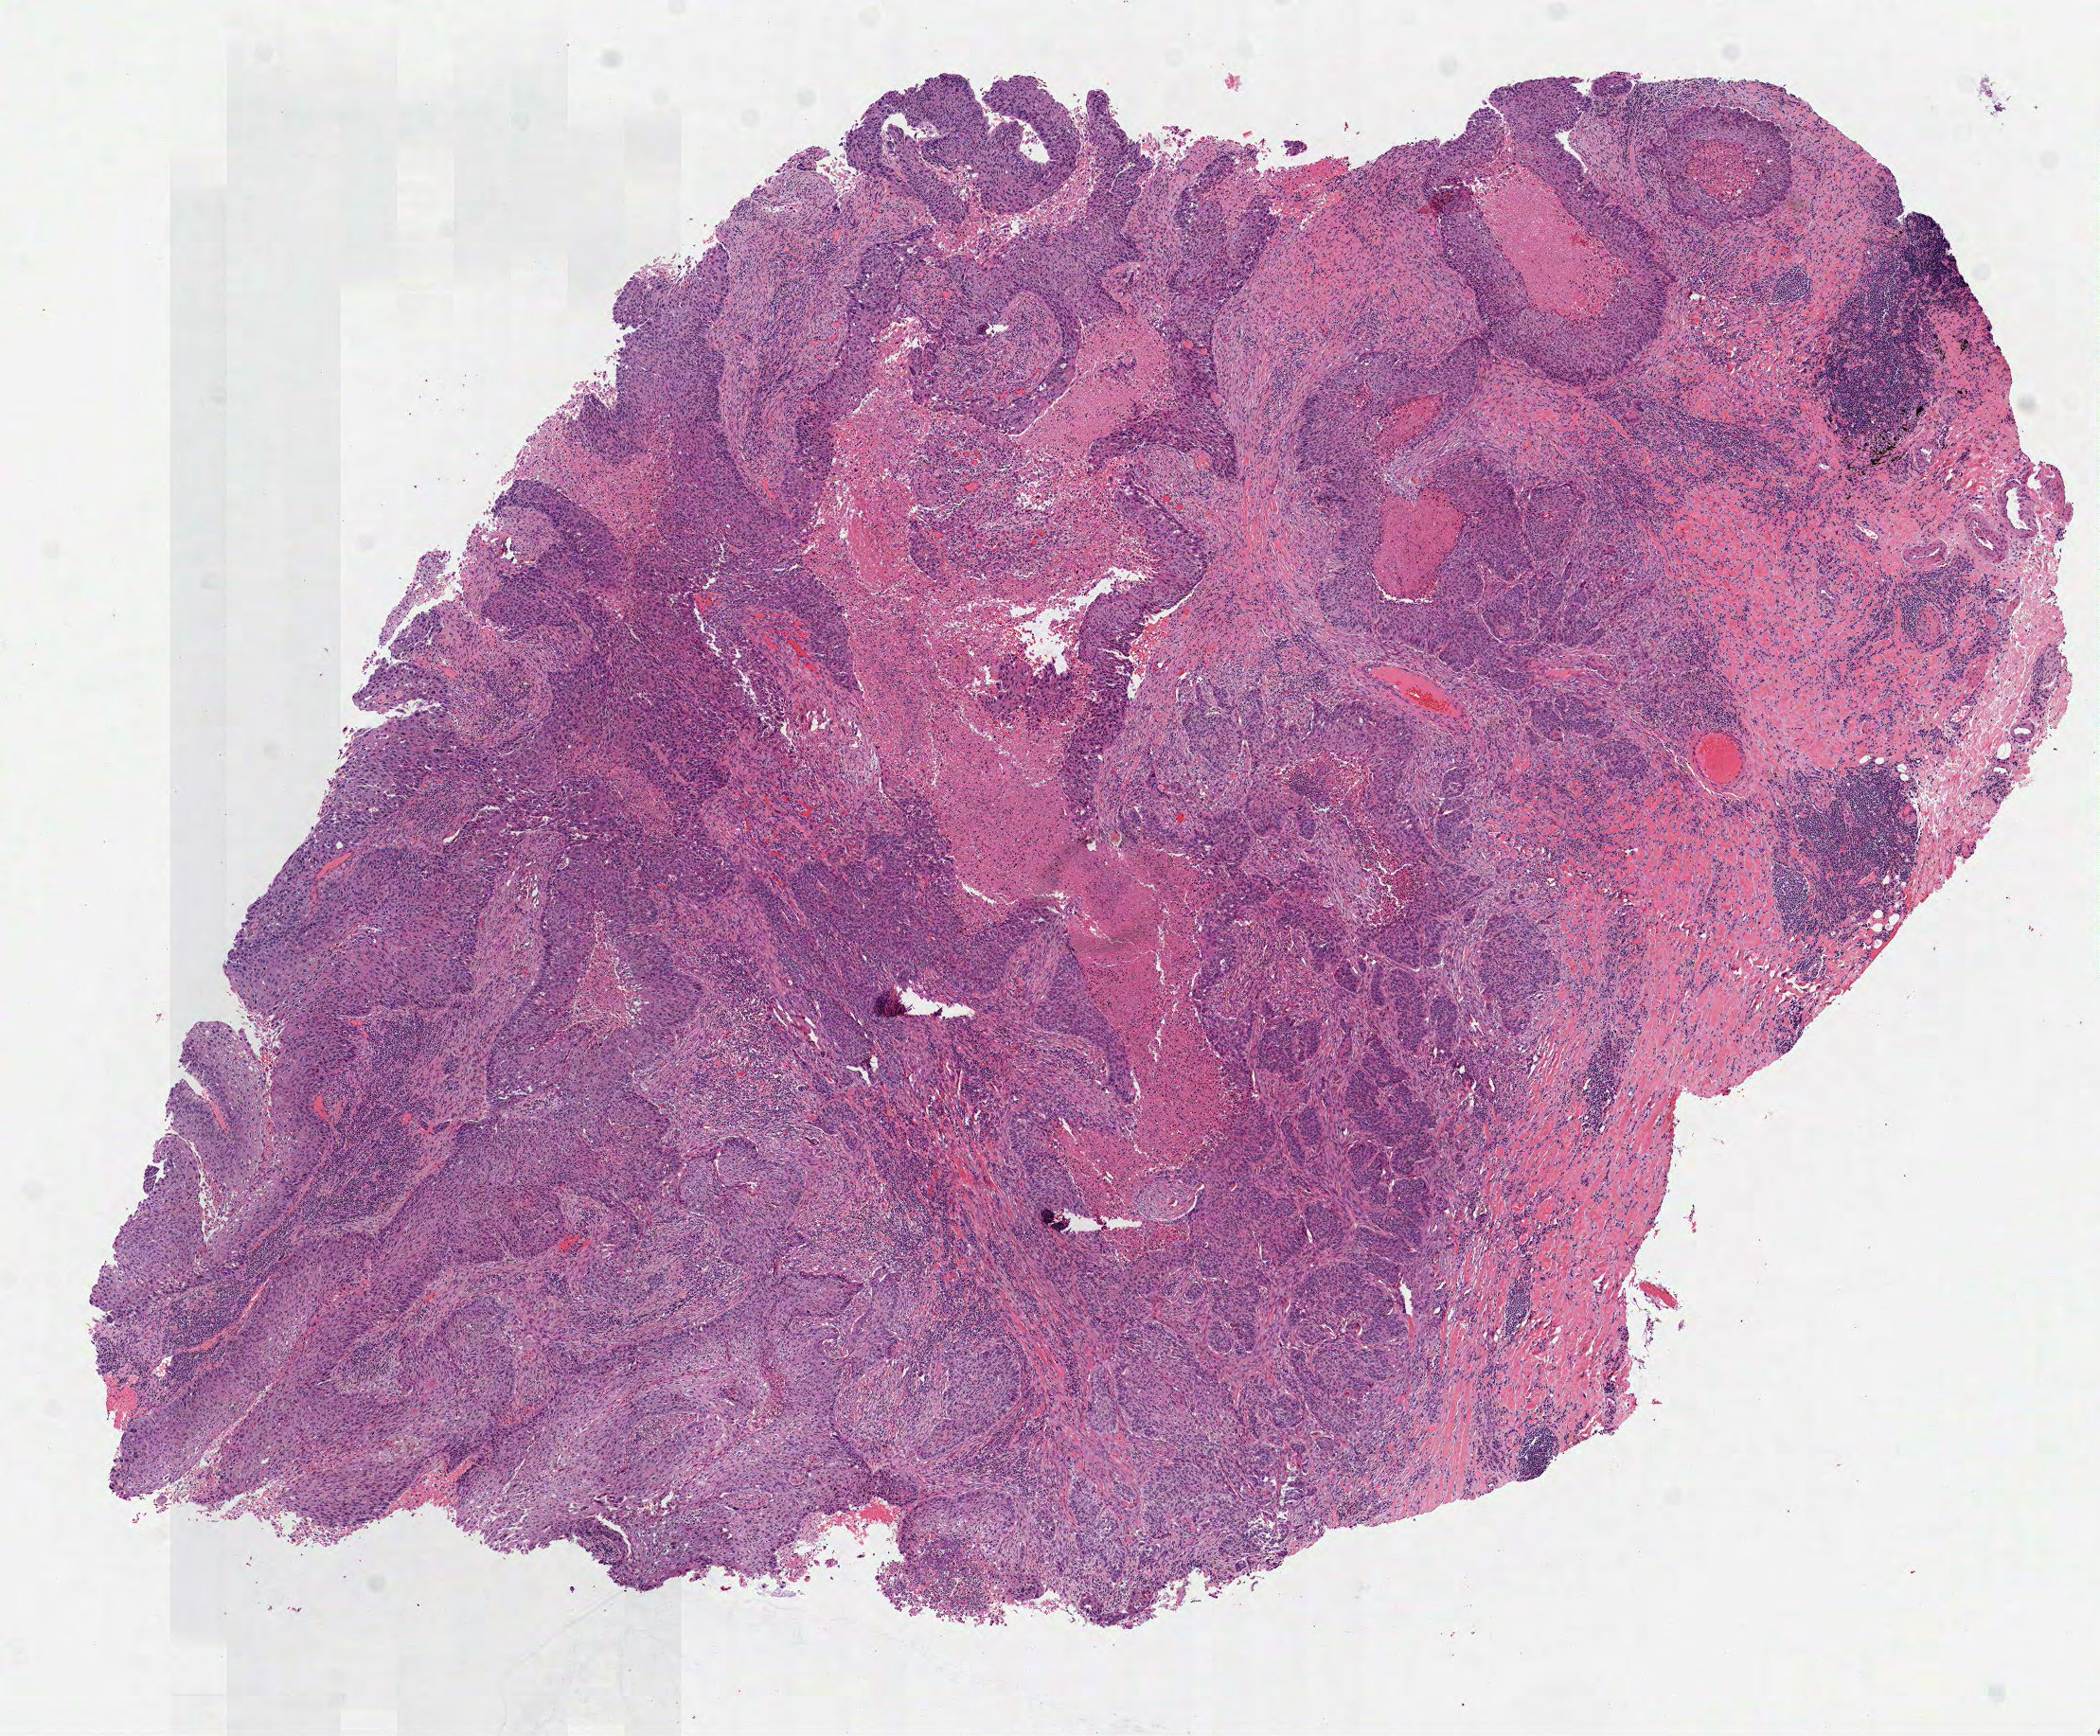
Digitized H&E-stained tissue section (whole slide), low-resolution overview of the scanned area, about 8.9 x 7.4 mm; frozen section from the top of the tissue portion; primary tumour sample from the lung. Patient: male, age at initial diagnosis 55 years.
Histologic diagnosis: Squamous cell carcinoma, NOS.